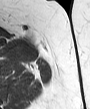
MRI of an extremity soft-tissue mass, one axial slice. Slice 29 of 45 in the series (ordered by position). MR volume resampled by the dataset authors to the PET/CT grid (not the native acquisition matrix). 90 × 109 image matrix, field of view 88 × 106 mm. Female patient. From the clinical record (not read from this slice): histological type: leiomyosarcoma; grade: intermediate; site of the primary tumour: parascapusular.
Outlined on this slice (expert contour drawn on MRI and transferred to this co-registered scan by the dataset authors):
- gross tumour volume including surrounding oedema: bounding box (x1, y1, x2, y2) in pixels: (26, 35, 36, 44)
- gross tumour volume (mass): (28, 37, 34, 40)